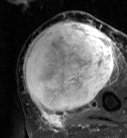
MRI of an extremity soft-tissue mass, one axial slice; T2-weighted fat-saturated; MR volume resampled by the dataset authors to the PET/CT grid (not the native acquisition matrix); 3.27 mm slice thickness; 127 × 138 image matrix, field of view 124 × 135 mm. Female patient. From the clinical record (not read from this slice): histological type: pleiomorphic leiomyosarcoma; grade: high; site of the primary tumour: left biceps.
Outlined on this slice (expert contour drawn on MRI and transferred to this co-registered scan by the dataset authors):
- gross tumour volume including surrounding oedema: bounding box (x1, y1, x2, y2) in pixels: (22, 20, 114, 113)
- gross tumour volume (mass): (22, 23, 114, 111)